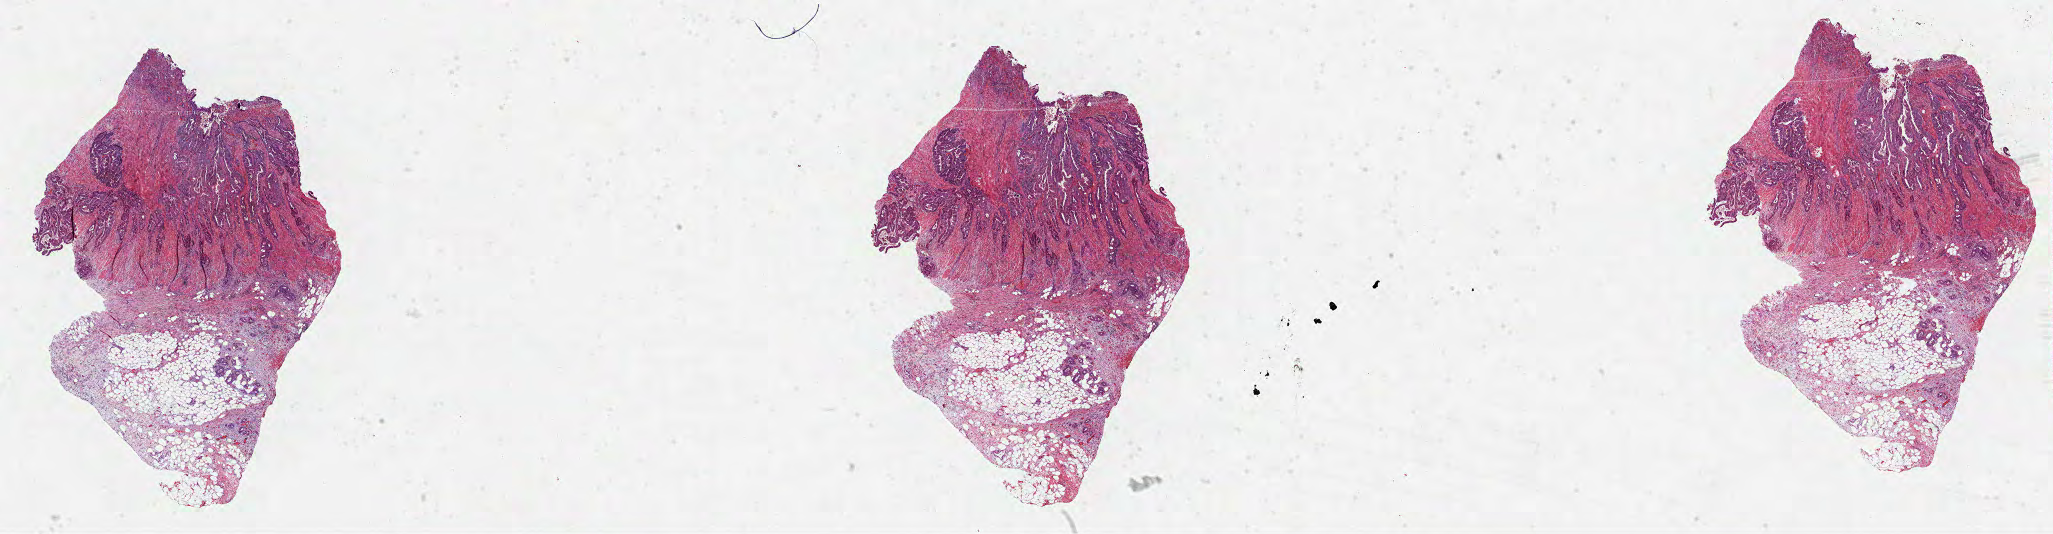
H&E whole-slide image — low-resolution overview of the scanned area, about 33.1 x 8.6 mm (slide scanned at 40x), formalin-fixed paraffin-embedded (FFPE) diagnostic section, colon, primary tumour sample. Female patient; age at initial diagnosis 56 years.
Lymph nodes positive (case pathology): 1 of 37 examined. AJCC pathologic stage: IVA (7th edition). Pathologic diagnosis: Adenocarcinoma, NOS (sigmoid colon).